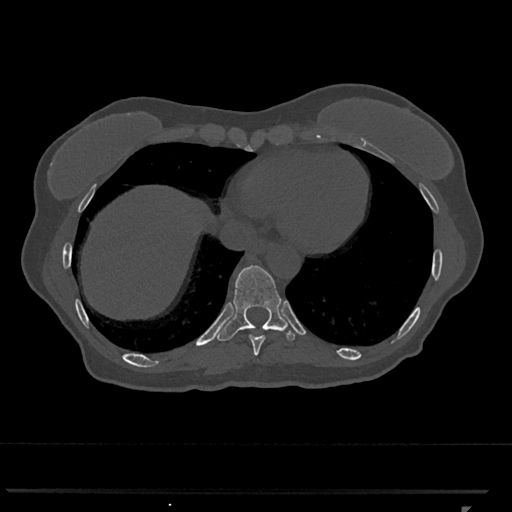
CT including the spine, one axial slice; position 586 of 793 along the scan axis; reconstruction kernel Br40s/3; bone window (W 1800 / L 400 HU); 0.5 mm slice thickness; 512 × 512 image matrix, field of view 380 × 380 mm. Female patient, age 62 years. Case-level facts recorded for this patient, not image findings: primary cancer: renal.
Annotated regions visible in this slice (semi-automatically segmented with operator editing):
- T10 vertebra: box from (x=217, y=265) to (x=295, y=341) px
- T9 vertebra: (x=249, y=335)–(x=266, y=356)